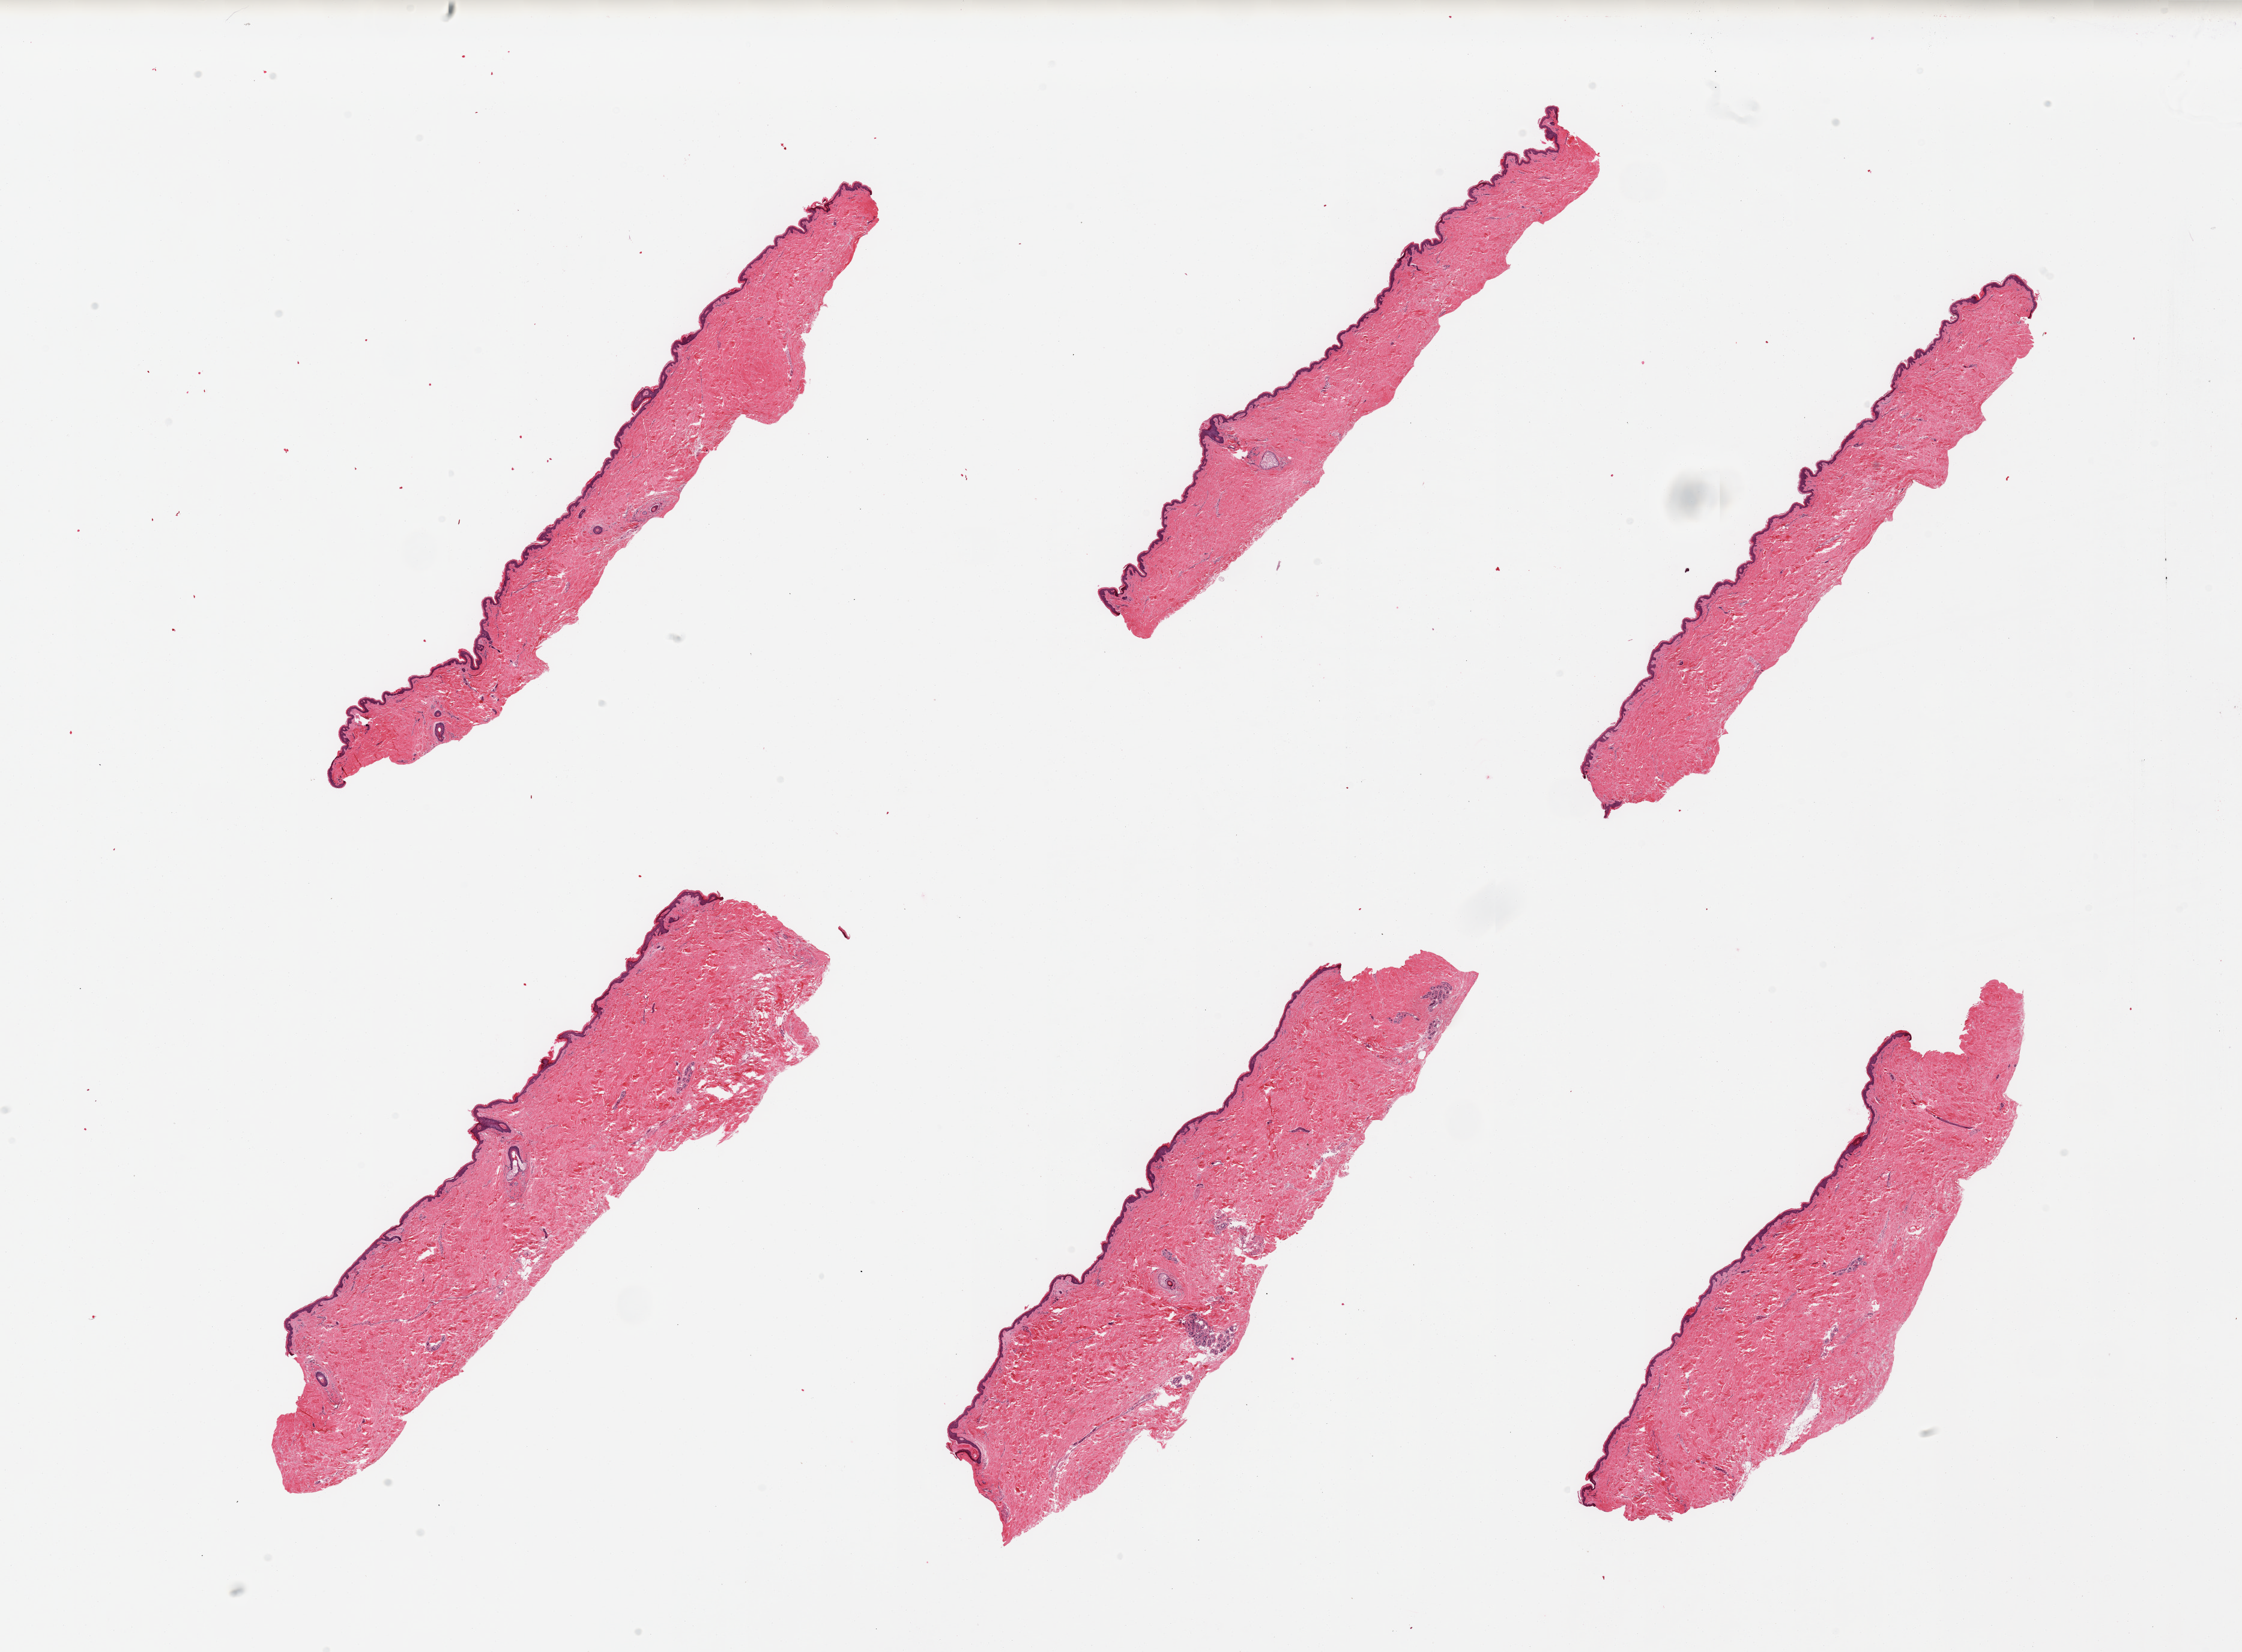
Whole-slide image, haematoxylin and eosin stain, low-resolution overview of the scanned area, about 29.5 x 21.8 mm; PAXgene-fixed paraffin-embedded (PFPE) section; section of skin of suprapubic region (target tissue); donor tissue sample.
Pathologist's review note for this sample: 6 pieces, minimal dermal fat; squamous epithelium is ~40-50 microns.